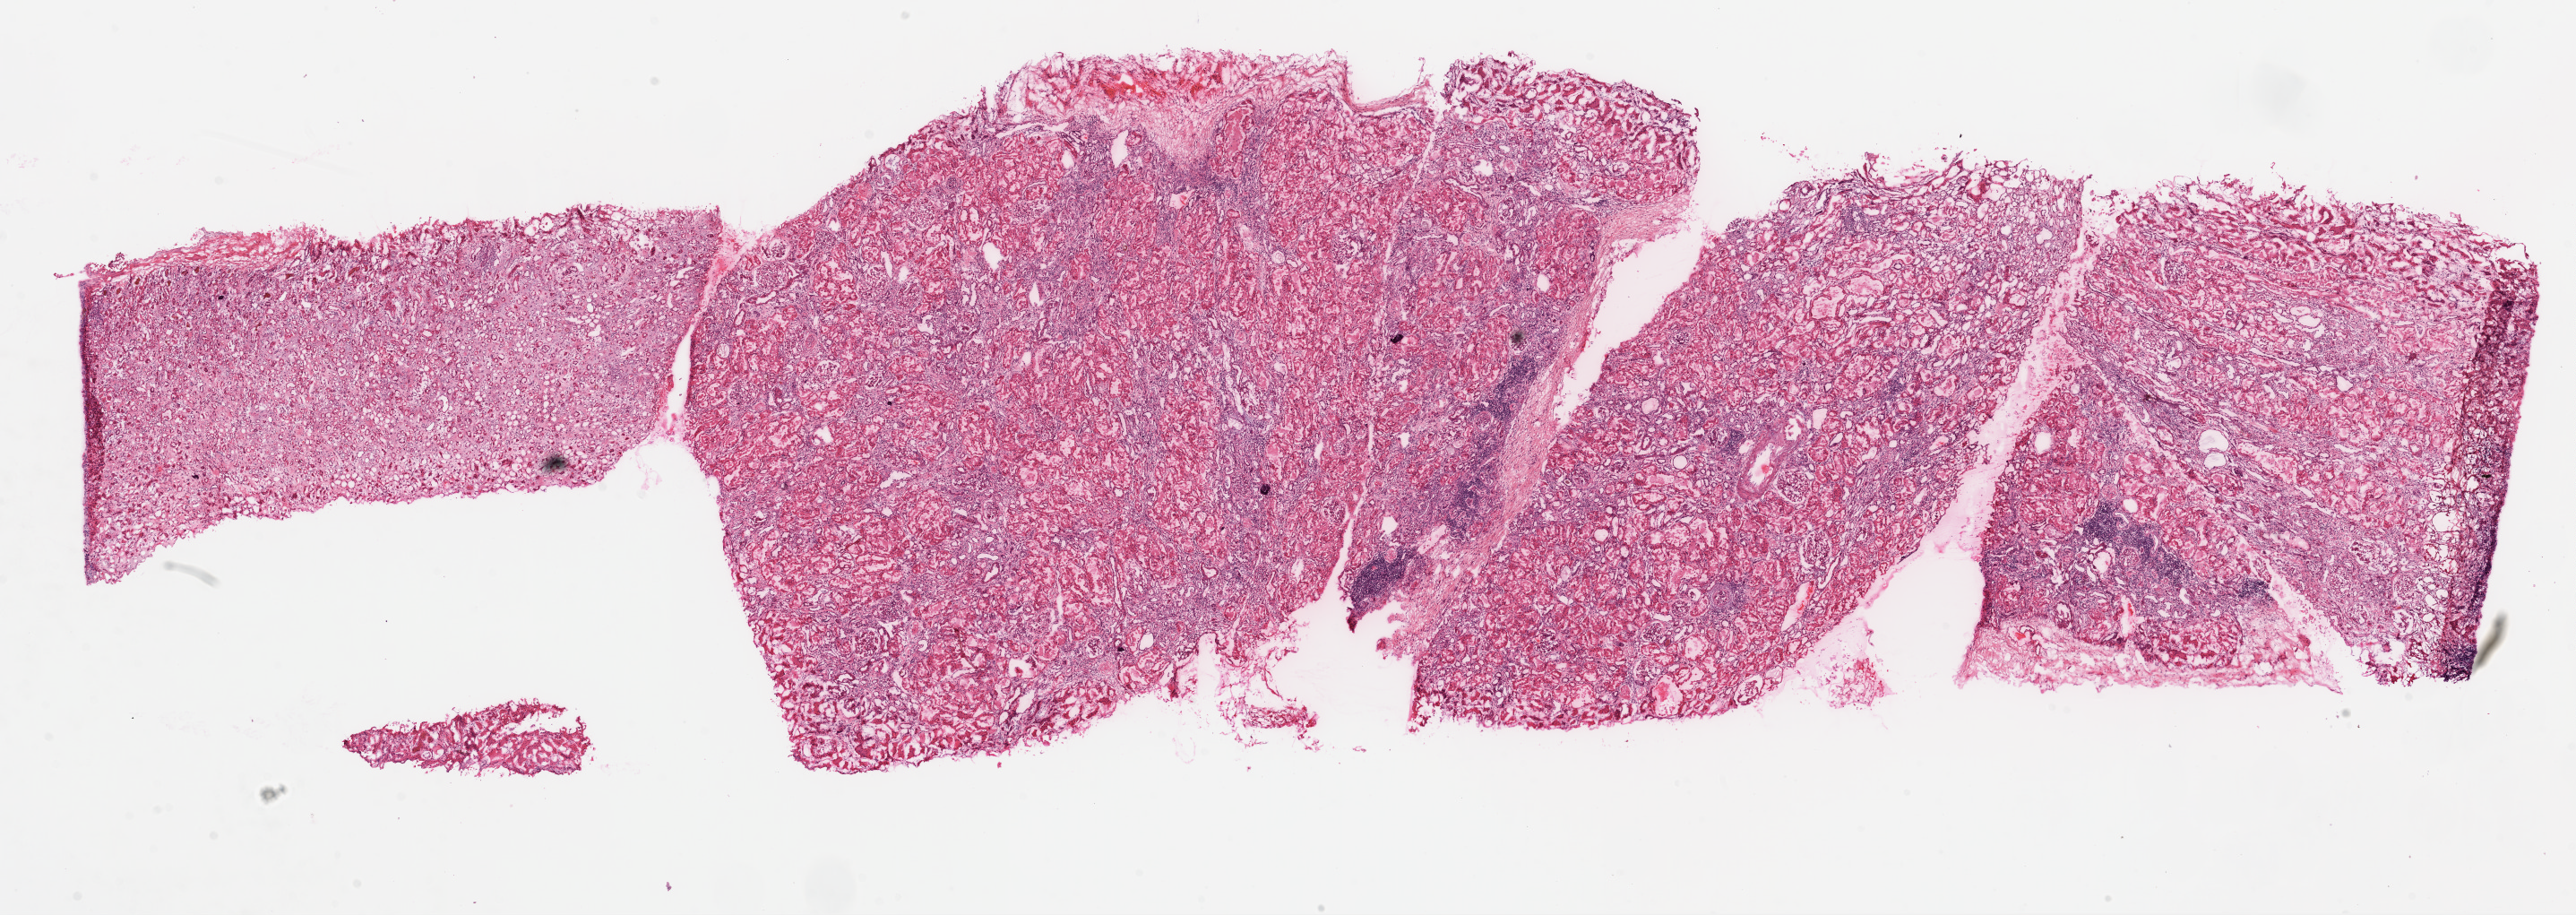
Hematoxylin and eosin (H&E) stained whole-slide image, shown as a low-resolution overview of the whole scanned area (about 23.1 x 8.2 mm, acquisition: 20x scan). Frozen section from the top of the tissue portion. Solid tissue normal (non-tumour tissue) sample from the kidney. Female, age 69 years at initial diagnosis.
This section: solid tissue normal (non-tumour) sample from the same patient. Patient diagnosis: Clear cell adenocarcinoma, NOS.